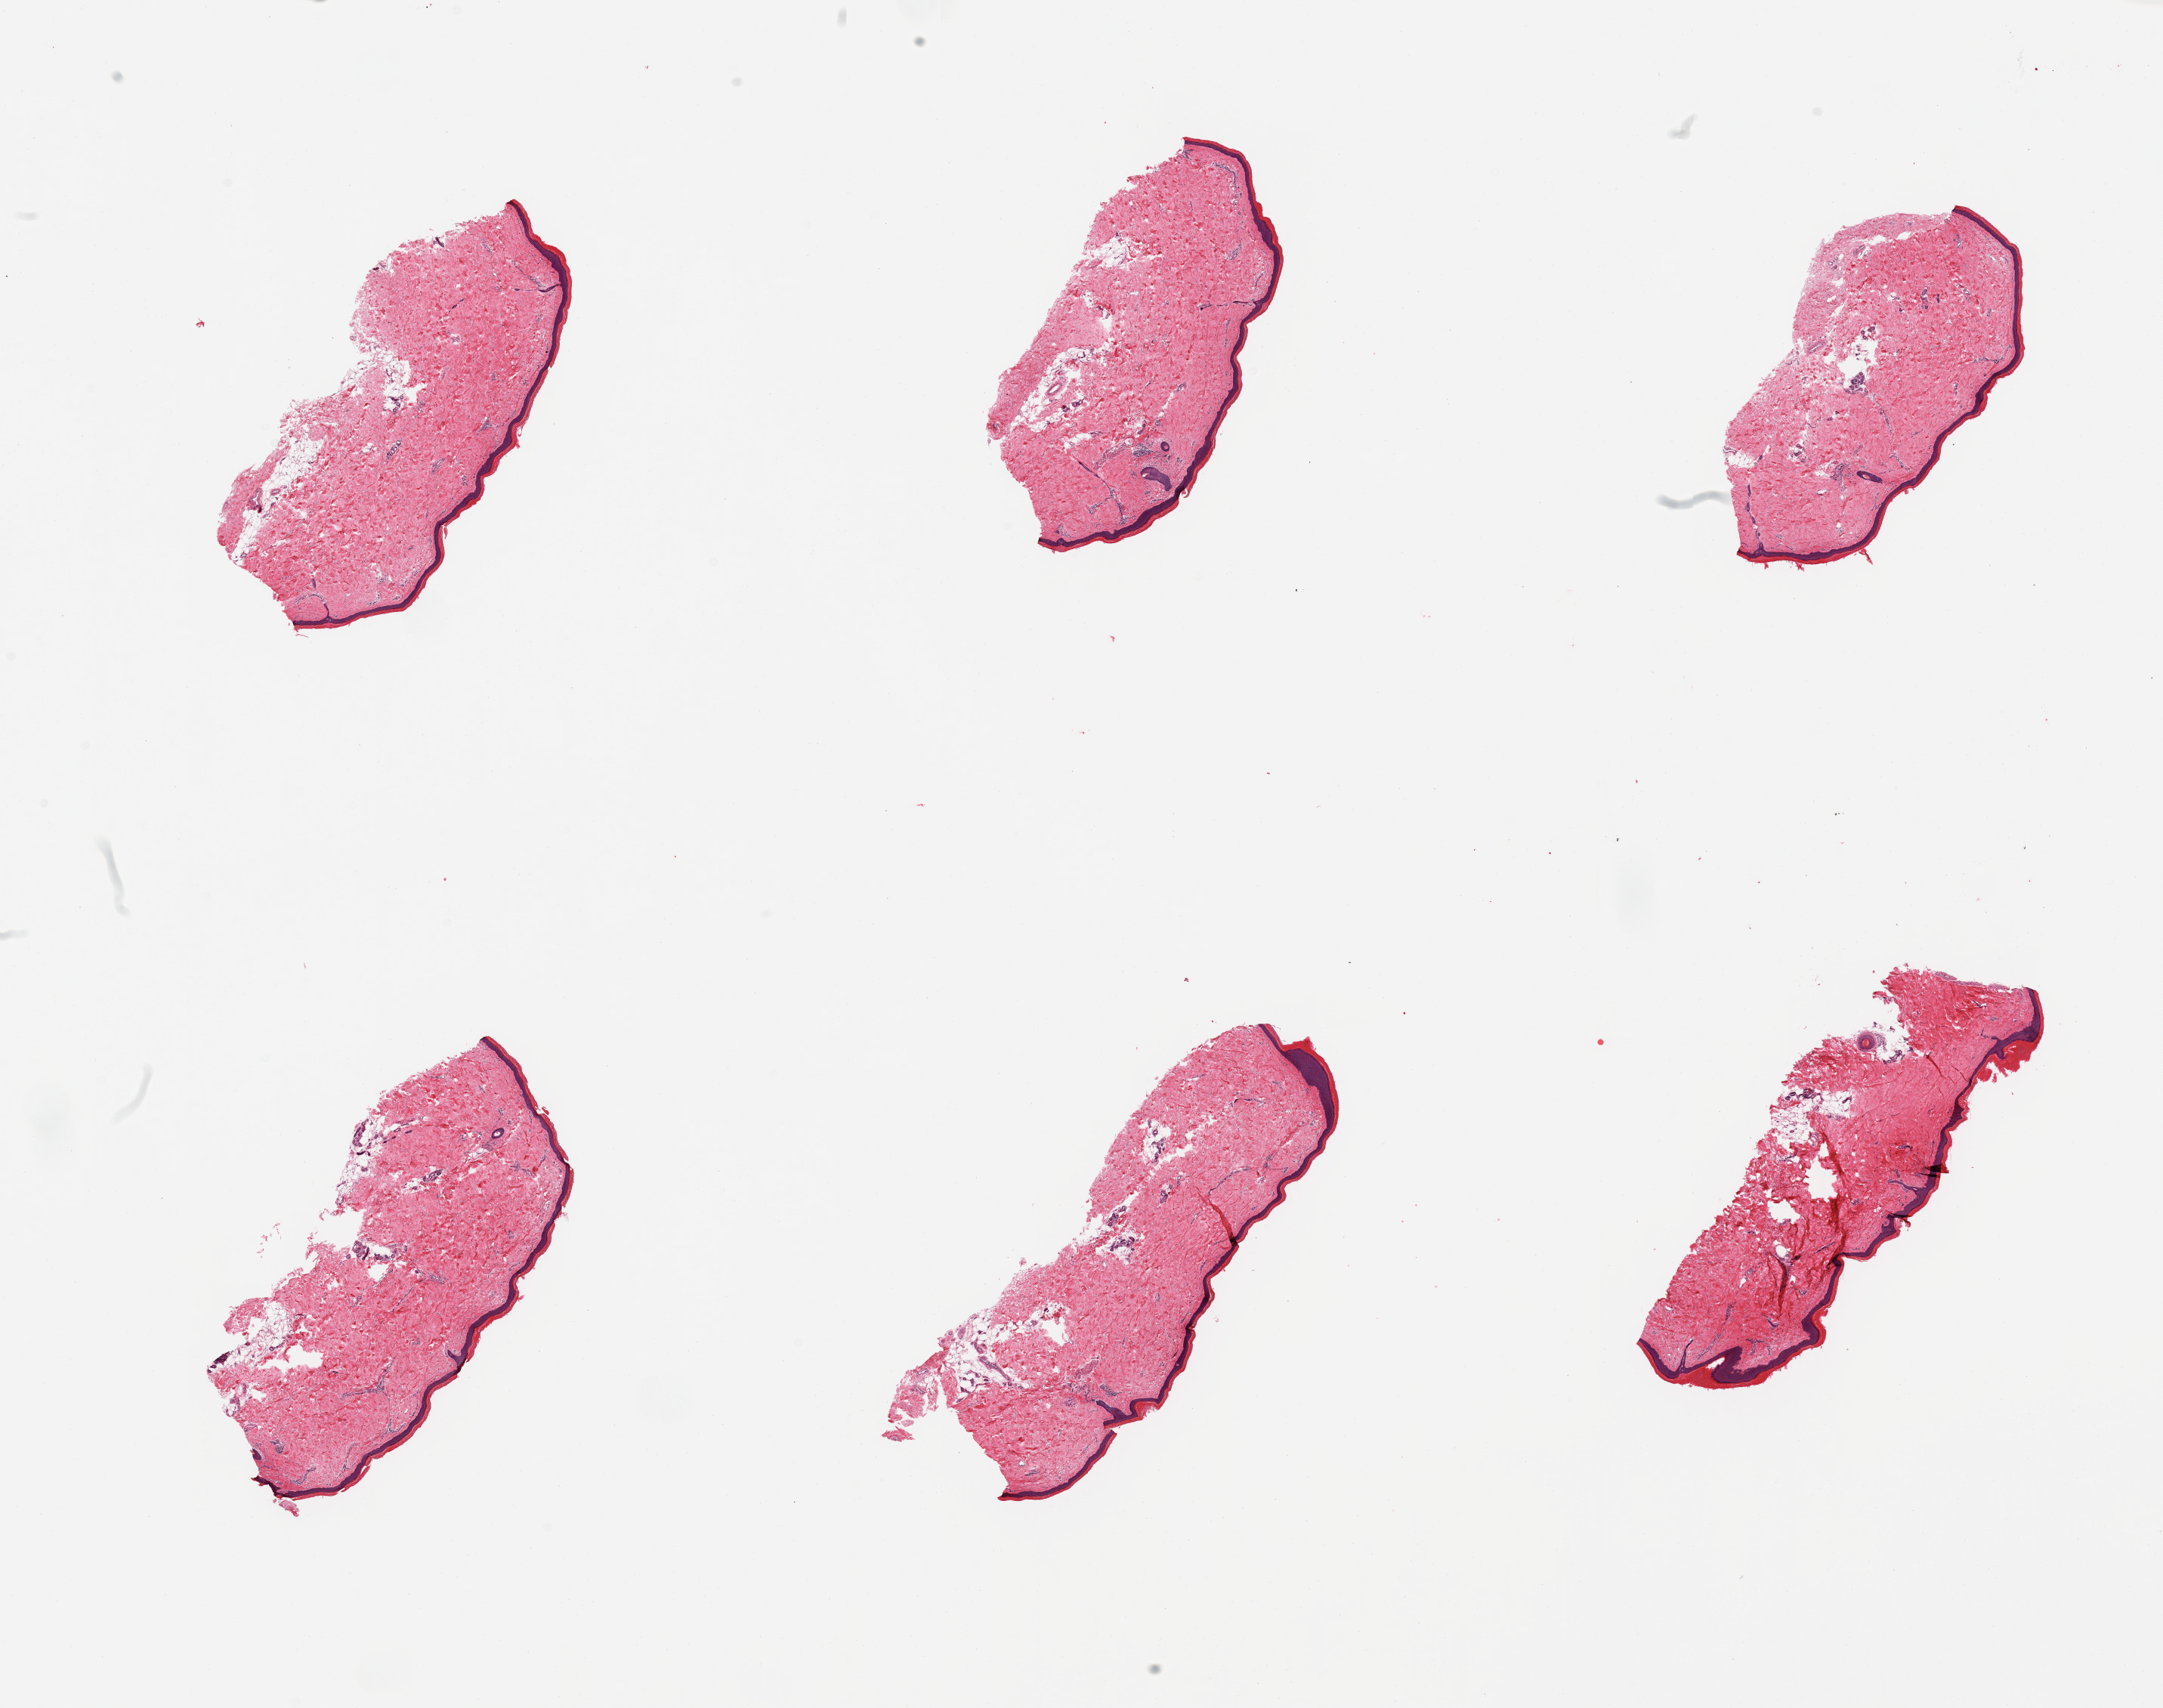
Hematoxylin and eosin (H&E) whole-slide image — whole scanned area (about 22.6 x 17.9 mm, from a 20x scan) shown as a low-resolution overview. PAXgene-fixed, paraffin-embedded tissue. Sampled site (target tissue): skin of lower leg. Tissue donor sample. Donor: female.
• review note (as recorded): 6 pieces; ~5% internal/periadnexal fat, epidermis ~40 microns thick